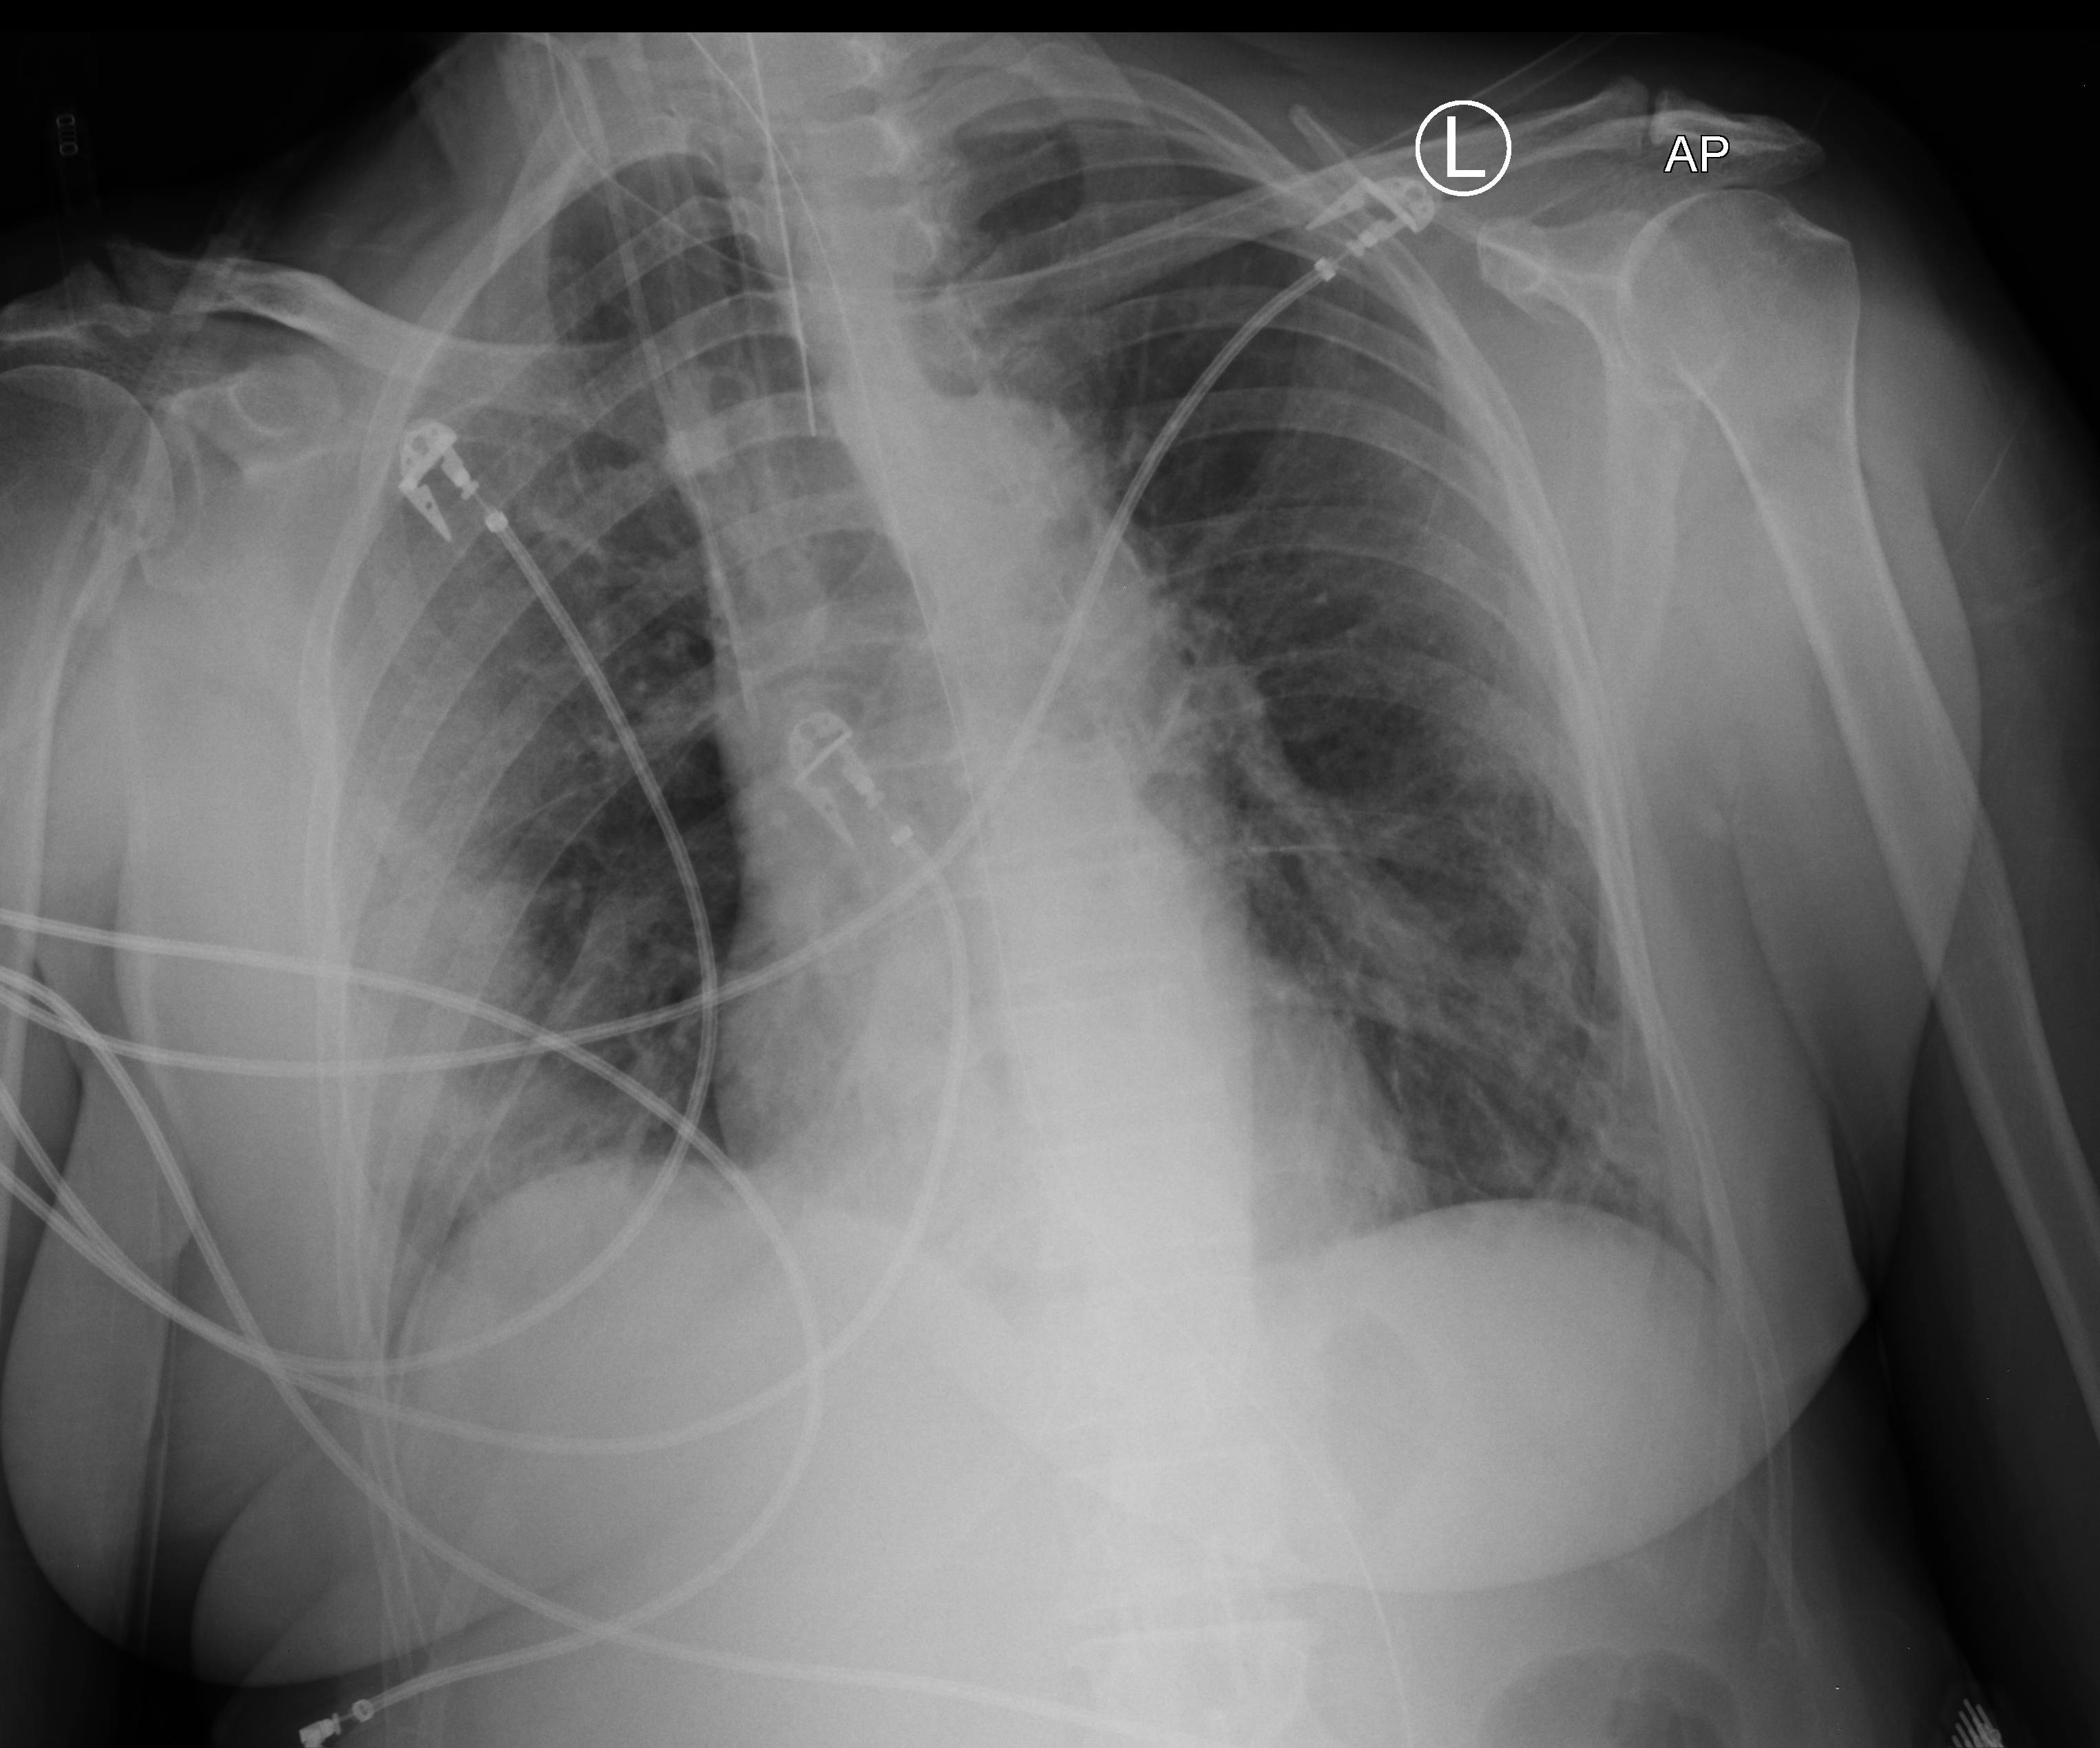
Bedside chest radiograph (computed radiography), anteroposterior (AP) projection. Patient hospitalised with COVID-19; female, aged 60–74 years.
From the hospital-stay record, not from the radiograph (when in the stay this image was taken is not recorded):
- mechanically ventilated during this hospital stay: yes